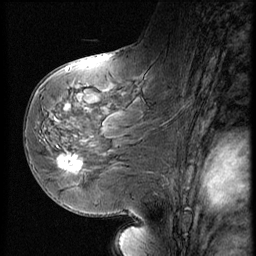
Breast MRI (dynamic contrast-enhanced), one sagittal slice; slice 28 of 56 in the series (ordered by position); dynamic contrast-enhanced series, image 2 of 3 at this slice position (ordered by acquisition); 1.5 T; TE 4.2 ms, TR 9 ms; 2.5 mm slice thickness; 256 × 256 image matrix, field of view 180 × 180 mm. Patient: female, 58 years. From the clinical record (not read from this slice): setting: breast cancer imaged before/during neoadjuvant chemotherapy; receptor status: HR-positive, HER2-negative.
Annotated regions visible in this slice (semi-automatic segmentation, software-assisted and operator-edited):
- analysis volume of interest (the breast-tissue region the enhancement analysis was run in; not a lesion): bounding box [x1, y1, x2, y2] px = [51, 147, 96, 185]
- tumour enhancement mask (voxels above the 140 % enhancement threshold inside the analysis volume of interest): [59, 155, 83, 173]